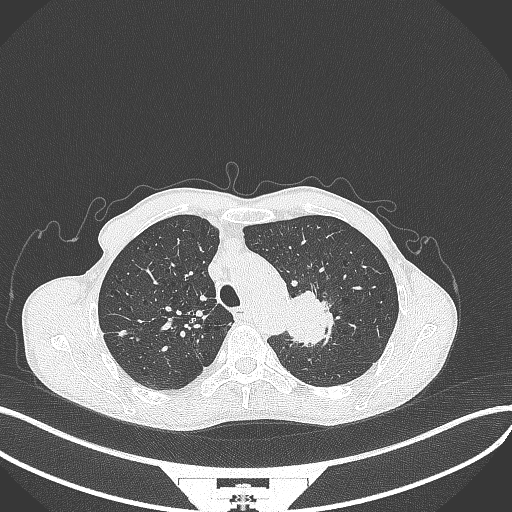
Chest CT, one axial slice; slice 320 of 386 in the series (ordered by position); reconstruction kernel B70f; 120 kVp; lung window (W 1500 / L -600 HU); 1 mm slice thickness; 512 × 512 image matrix. Patient: male, 65 years. From the clinical record (not read from this slice): clinical TNM (as recorded): T2b N0 M0; histopathological grade: G2.
Outlined on this slice (rectangle marked by the reading radiologist):
- lung tumour (recorded histology: adenocarcinoma): bounding box [x1, y1, x2, y2] px = [285, 283, 336, 352]